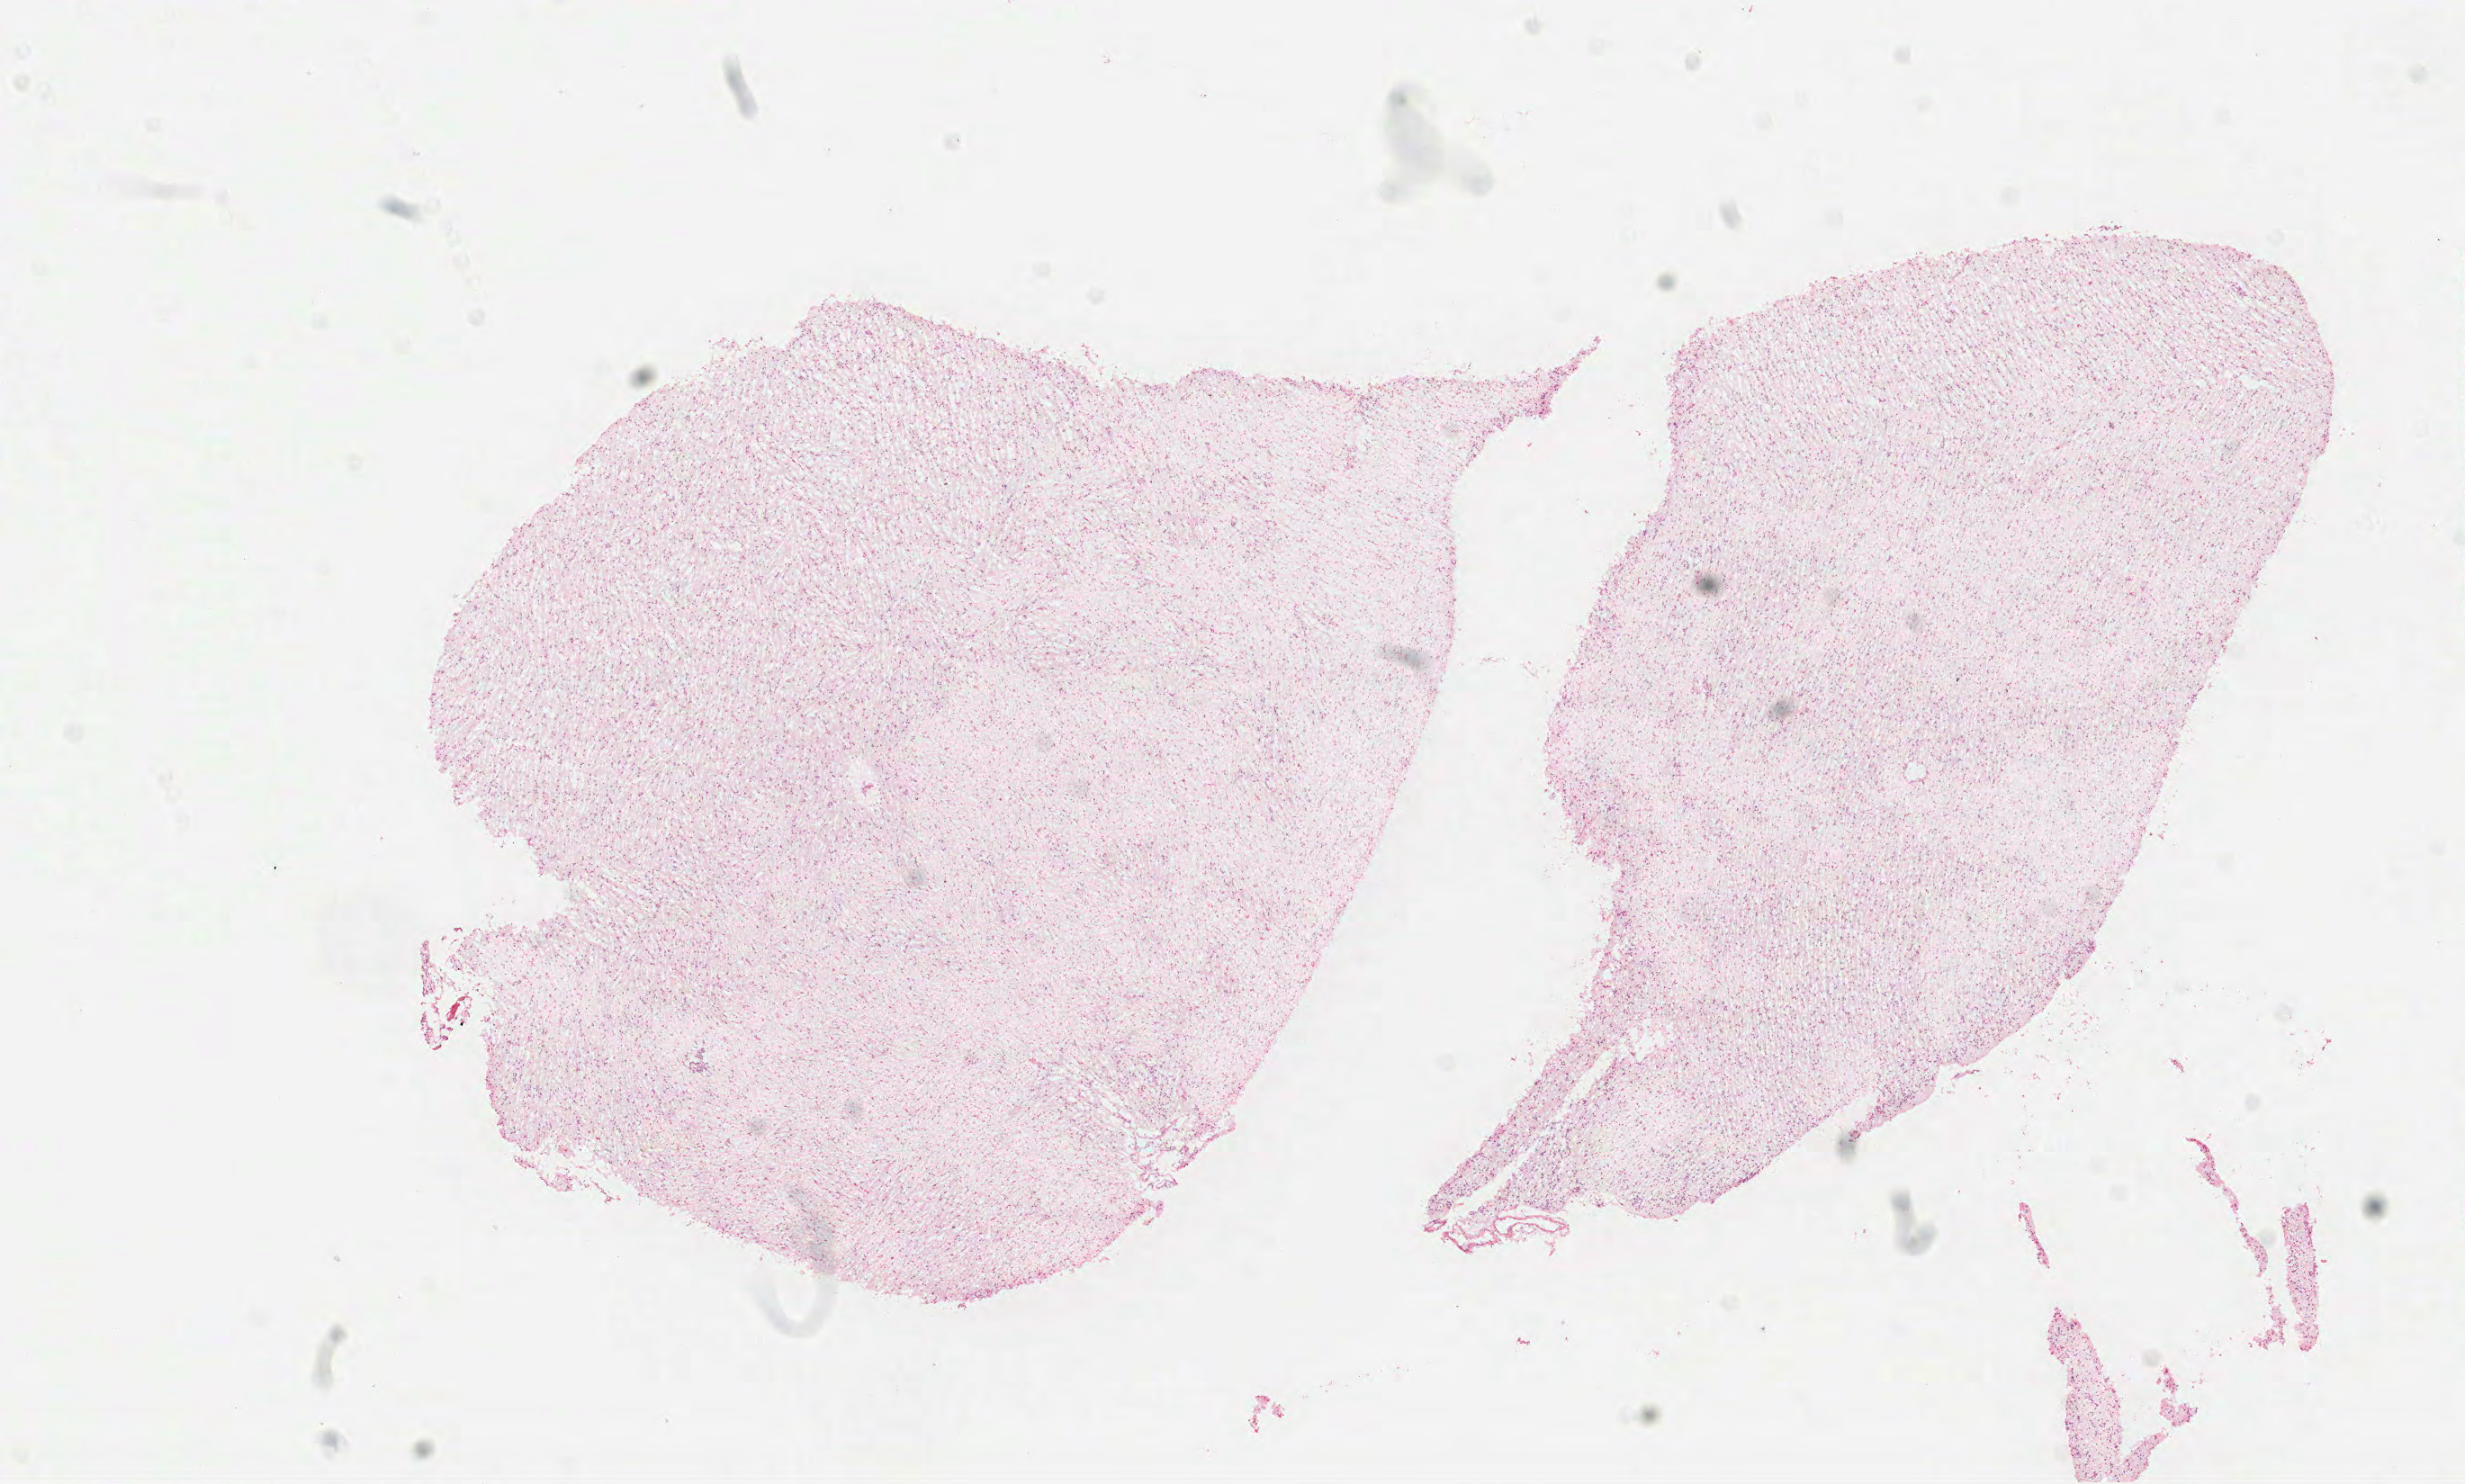
Hematoxylin and eosin (H&E) stained whole-slide image — whole scanned area (about 11.0 x 6.6 mm) shown as a low-resolution overview; frozen section from the top of the tissue portion; primary tumour sample from the brain. Female patient; age at initial diagnosis 42 years. Histologic grade: G3 (poorly differentiated). Pathologist review of this section (percent, as recorded): tumour cells 100%, tumour nuclei 75%, normal cells 0%, stromal cells 0%, necrosis 0%.
Pathologic diagnosis: Mixed glioma (cerebrum).